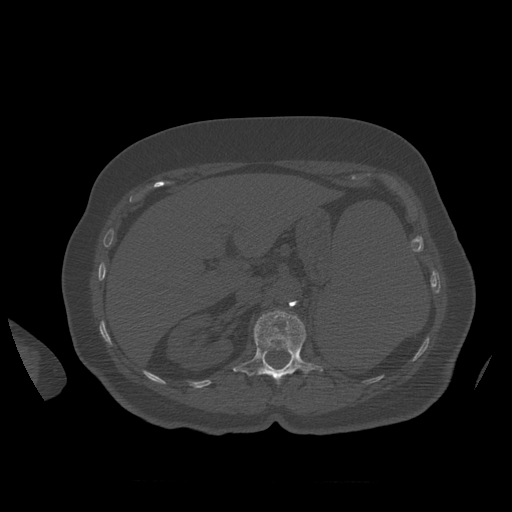
CT including the spine, one axial slice. Position 279 of 399 along the scan axis. Reconstruction kernel STANDARD. Bone window (W 1800 / L 400 HU). 1.25 mm slice thickness. 512 × 512 image matrix, field of view 404 × 404 mm. Patient age 81 years. Case-level facts recorded for this patient, not image findings: primary cancer: renal.
Outlined on this slice (semi-automatically segmented with operator editing):
- L1 vertebra: bounding box [x1, y1, x2, y2] px = [233, 310, 324, 385]